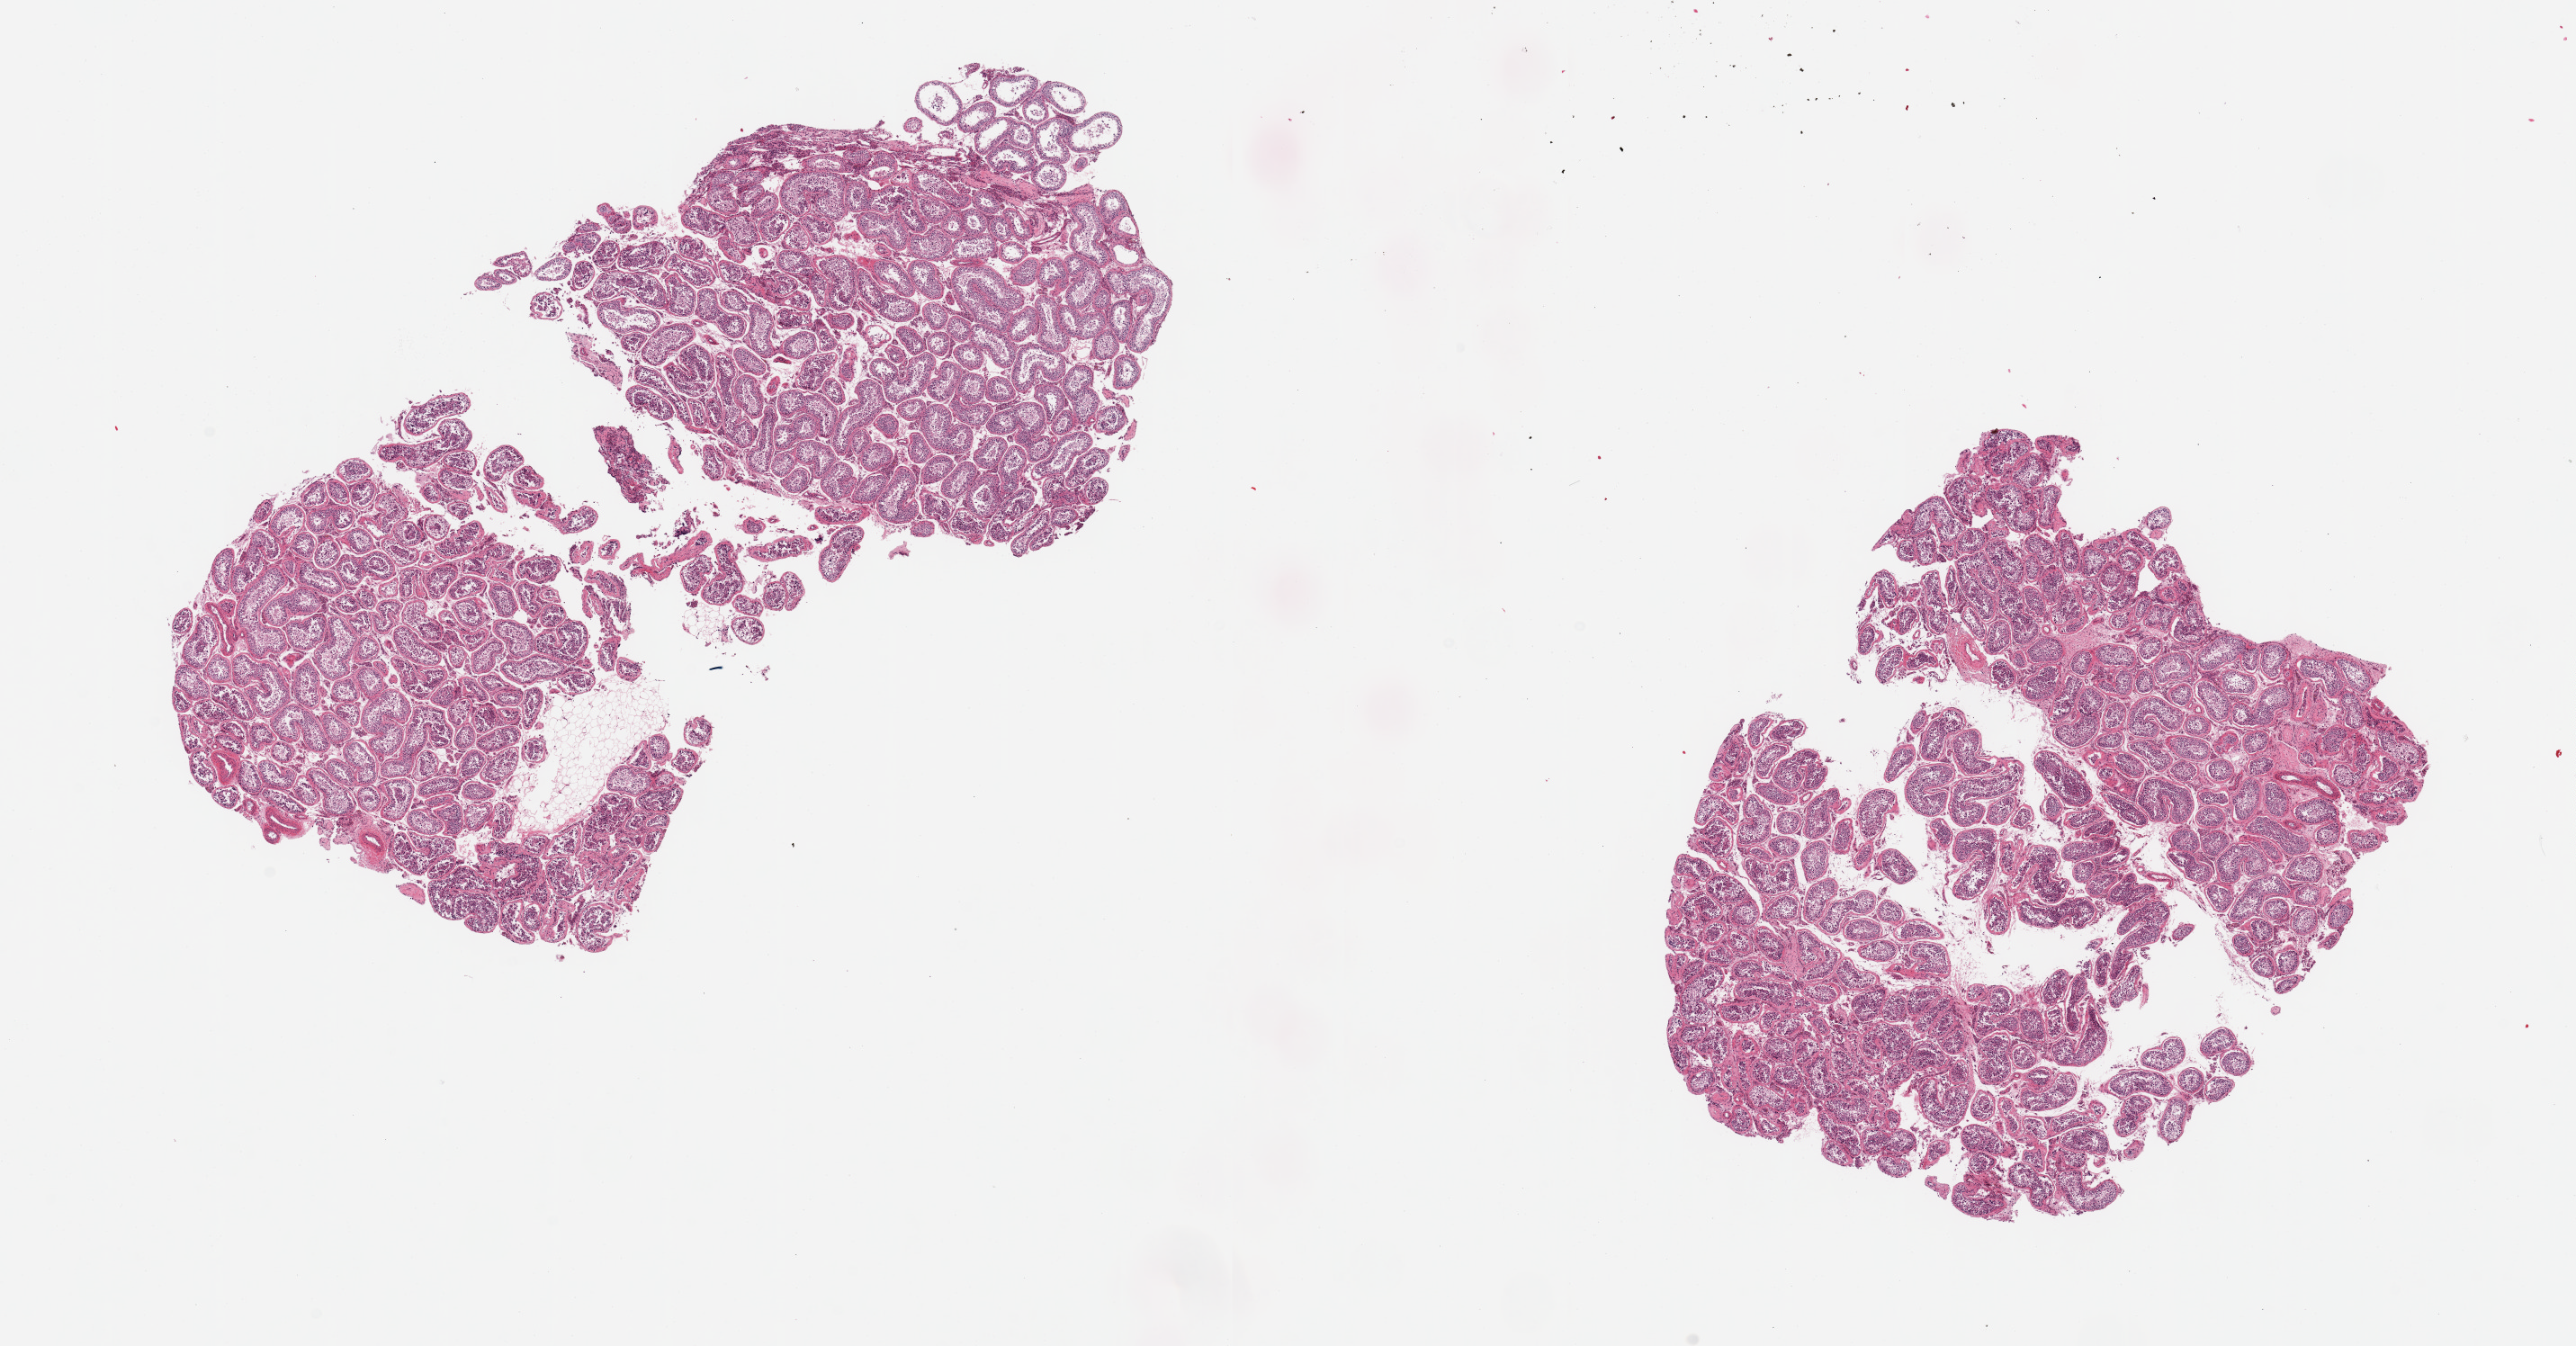
Digitized H&E-stained section, shown as a low-resolution overview of the whole scanned area (about 22.6 x 11.8 mm, slide scanned at 20x). PAXgene-fixed, paraffin-embedded tissue. Sampled site (target tissue): testis. Donor tissue sample. Male donor.
Pathologist's review note for this sample: 2 fragmented pieces; active spermatogenesis.